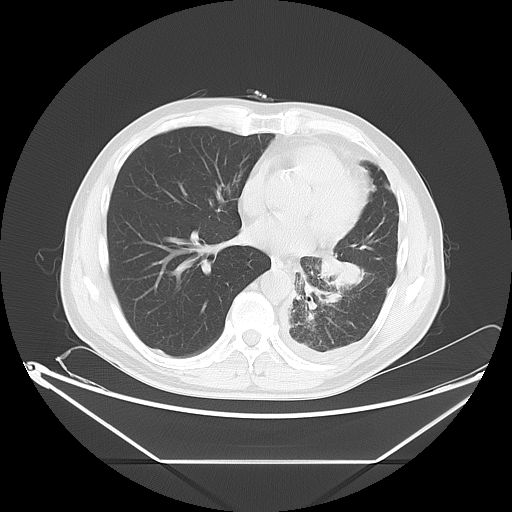
Chest CT, one axial slice. Position 28 of 63 along the scan axis. 120 kVp. Lung window (W 1500 / L -600 HU). 5 mm slice thickness. 512 × 512 image matrix. Patient: male, 60 years. Case-level facts recorded for this patient, not image findings: clinical TNM (as recorded): T4 N1 M1.
Annotated regions visible in this slice (rectangle marked by the reading radiologist):
- lung tumour (recorded histology: adenocarcinoma): bounding box <313,245,372,298> (left, top, right, bottom; pixels)